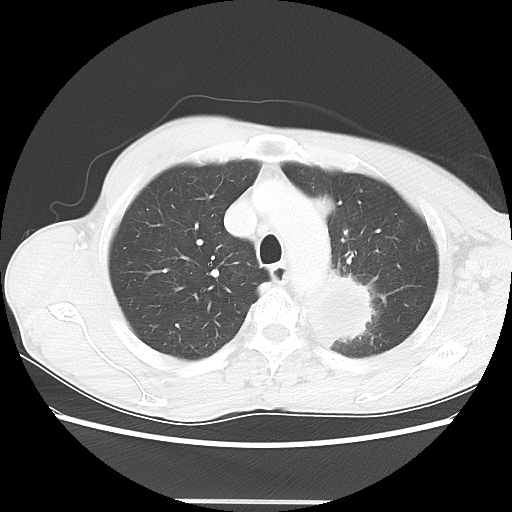
Chest CT, one axial slice. Slice 50 of 62 in the series (ordered by position). 100 kVp. Lung window (W 1500 / L -600 HU). 512 × 512 image matrix. Male patient, age 61 years. Case-level facts recorded for this patient, not image findings: clinical TNM (as recorded): T3 N1 M1.
Structures marked on this image (bounding box drawn by a radiologist):
- lung tumour (recorded histology: adenocarcinoma): bounding box [x1, y1, x2, y2] px = [301, 271, 375, 351]
- lung tumour (recorded histology: adenocarcinoma): [306, 188, 344, 222]